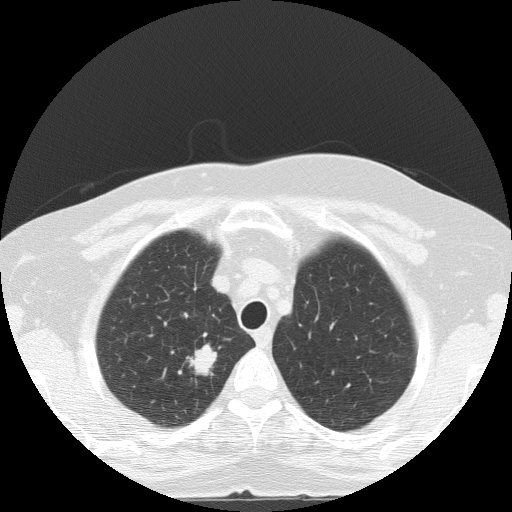
Low-dose screening chest CT, one axial slice. Position 111 of 133 along the scan axis. Reconstruction kernel FC51. 120 kVp. Lung window (W 1500 / L -600 HU). 2 mm slice thickness. 512 × 512 image matrix.
Outlined on this slice (expert manual segmentation):
- lesion 1 (tumor, upper lobe of right lung): bounding box (x1, y1, x2, y2) in pixels: (186, 343, 217, 376)